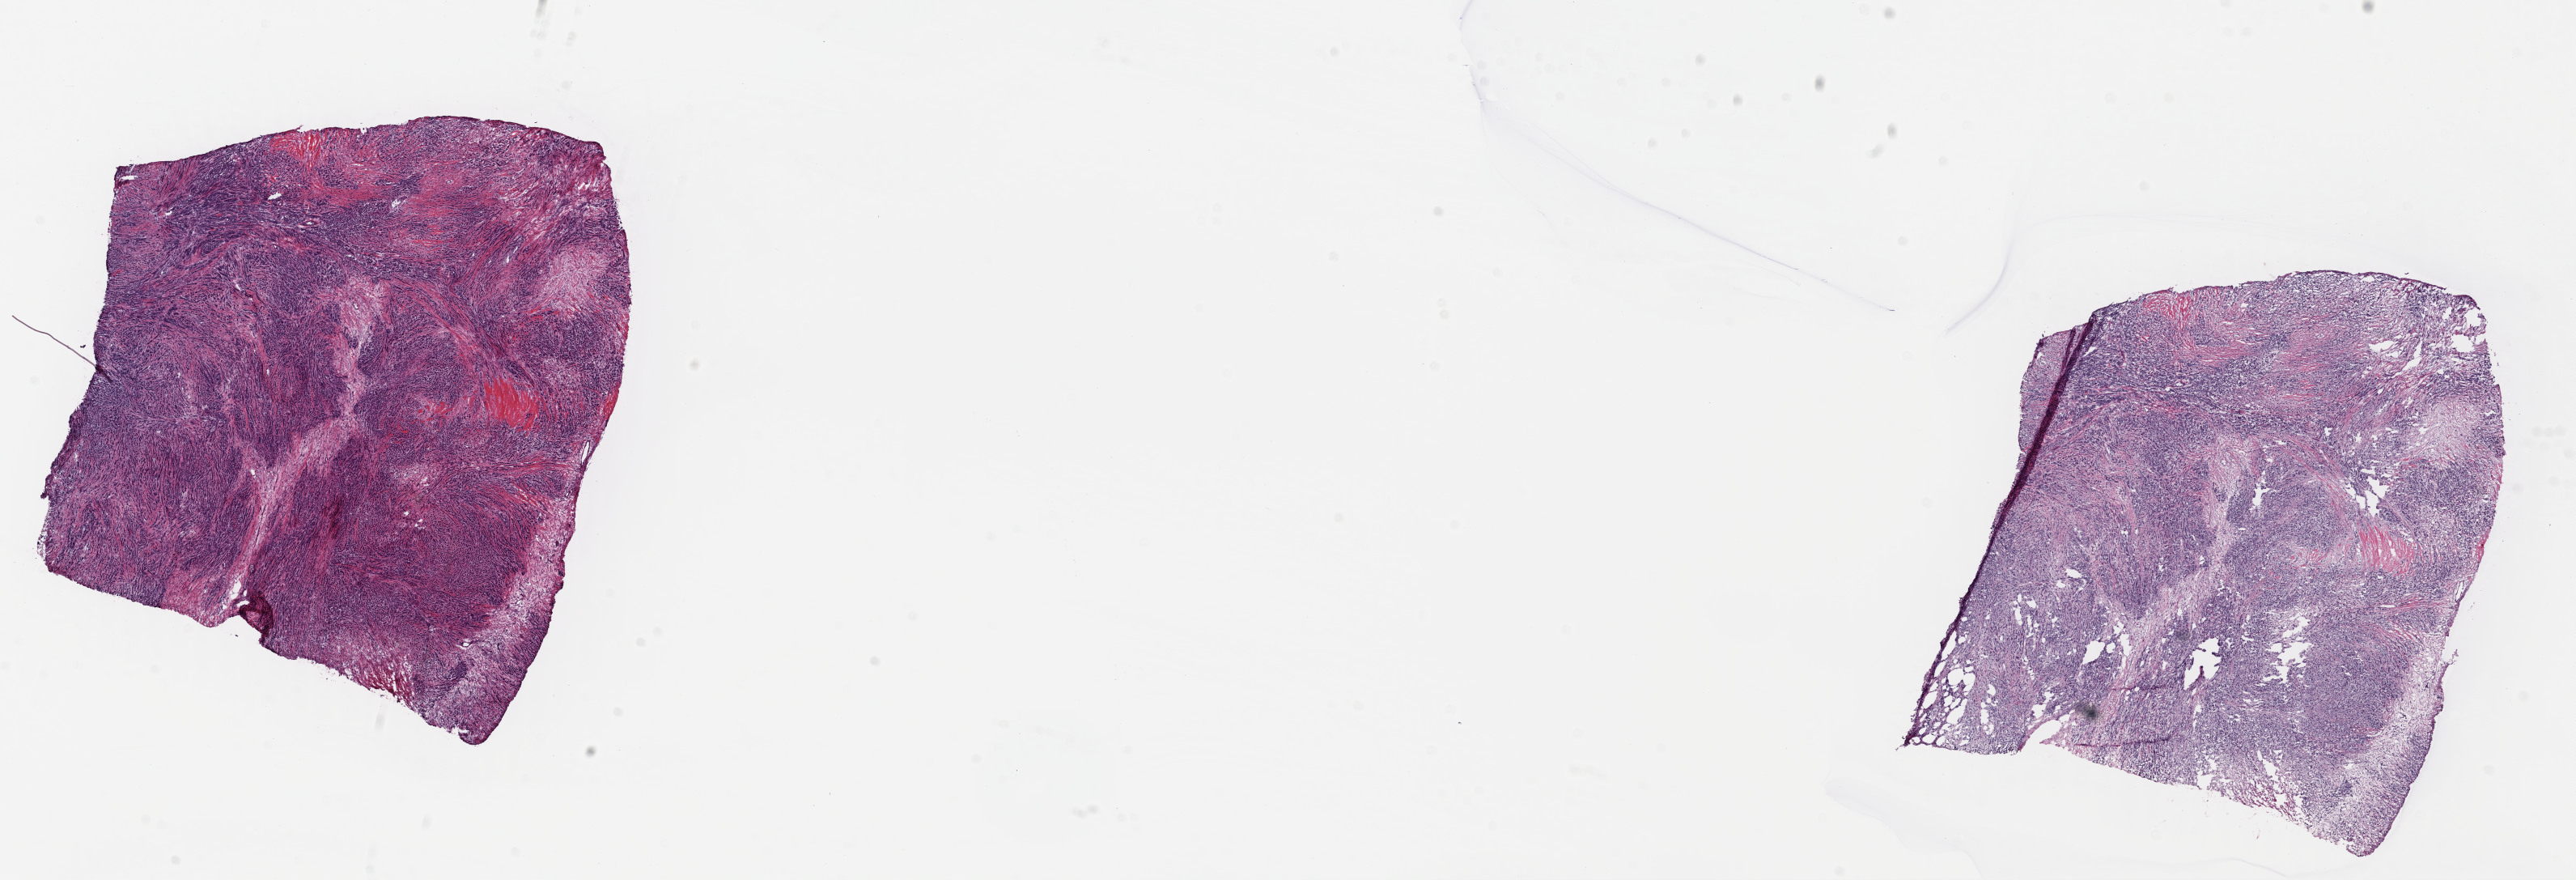
Whole-slide histology image, Hematoxylin and eosin (H&E) stained — shown as a low-resolution overview of the whole scanned area (about 25.0 x 8.5 mm). Frozen section from the top of the tissue portion. Breast, primary tumour sample. Female patient; age at initial diagnosis 80 years. Slide review estimates, as recorded: tumour cells 100%, tumour nuclei 90%, normal cells 0%, stromal cells 0%, necrosis 0%. Inflammatory infiltration, as recorded: lymphocyte infiltration 0%, monocyte infiltration 0%, neutrophil infiltration 0%.
Lymph nodes positive (case pathology): 1 of 22 examined. AJCC pathologic stage: IIIA. Histologic diagnosis: Infiltrating duct carcinoma, NOS.